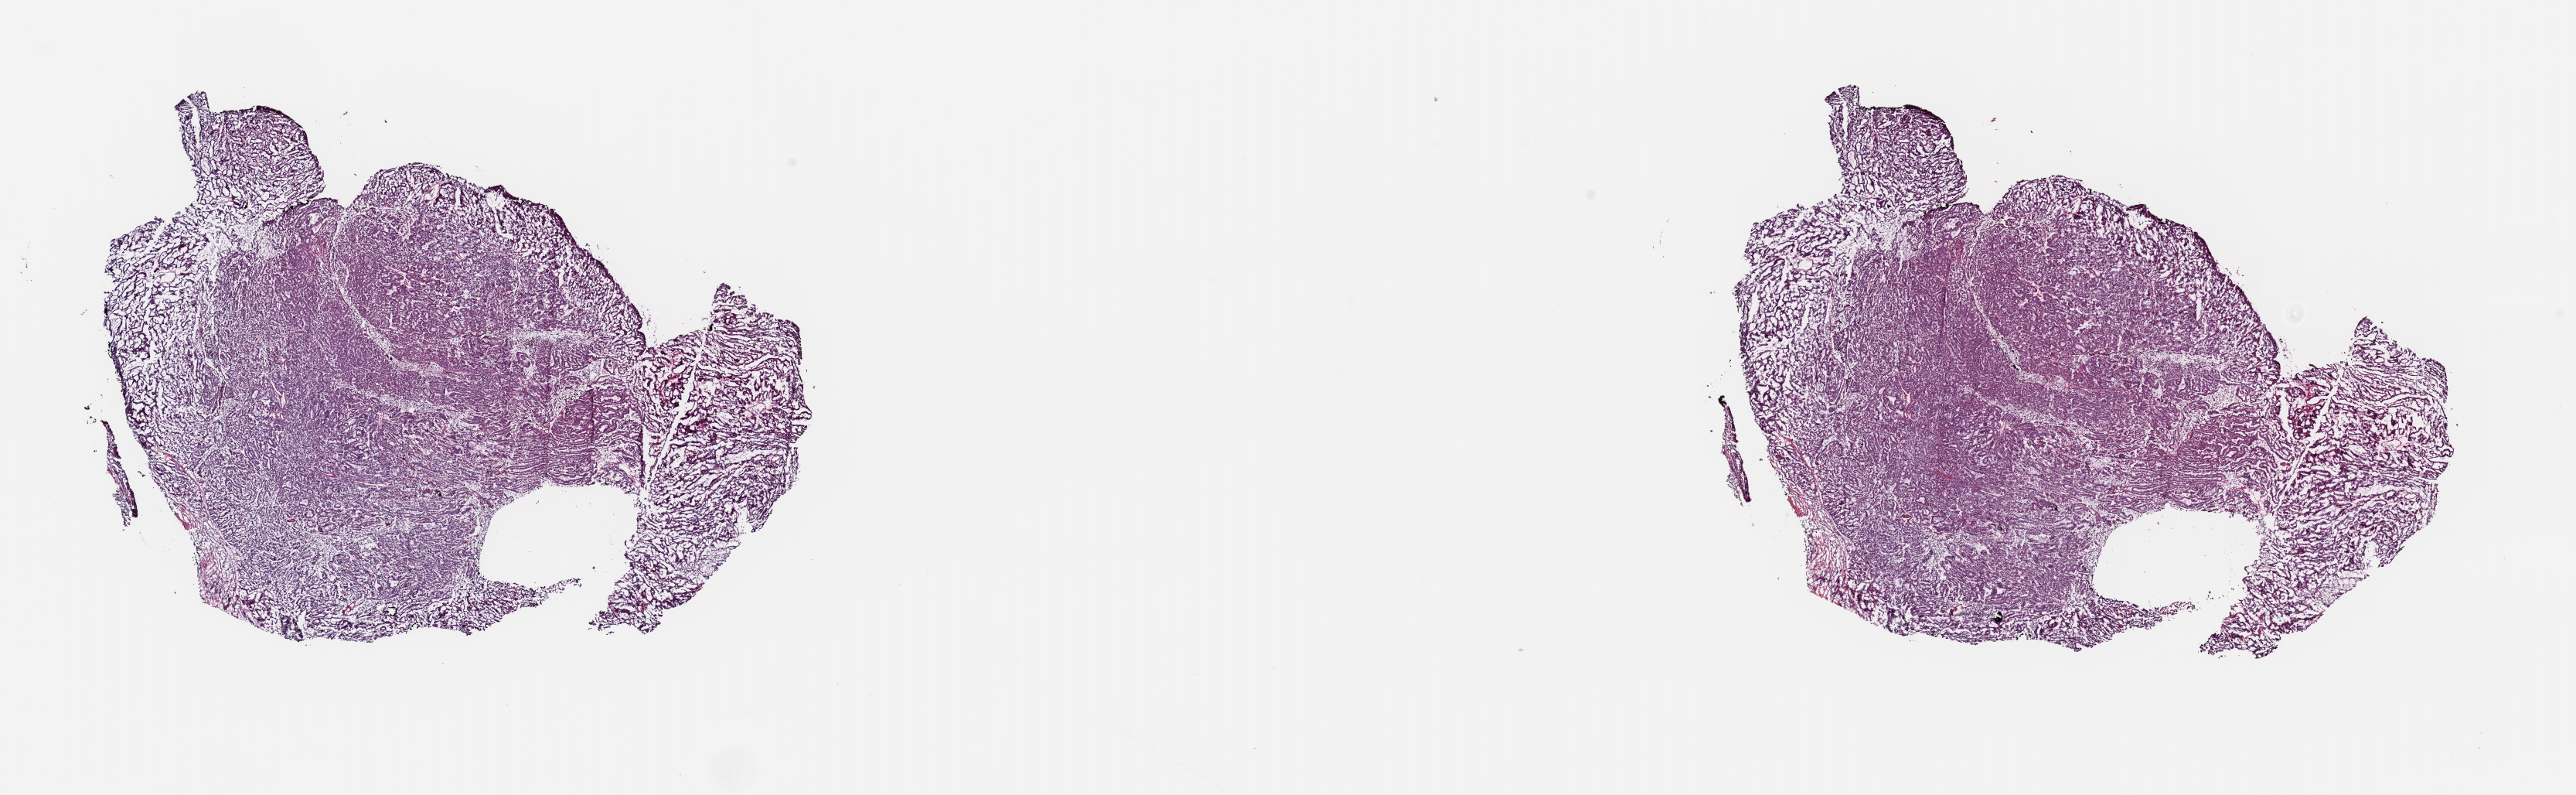
Digitized H&E-stained tissue section (whole slide), a low-resolution overview of the entire scanned area, about 26.3 x 8.1 mm (slide scanned at 40x), frozen section from the top of the tissue portion, sample: primary tumour, thyroid. Patient: female, age at initial diagnosis 33 years. Slide review estimates, as recorded: tumour cells 100%, tumour nuclei 97%, normal cells 0%, stromal cells 0%, necrosis 0%. Infiltration values recorded for this section: lymphocyte infiltration 0%, monocyte infiltration 0%, neutrophil infiltration 0%.
AJCC pathologic stage: I (6th edition). Laterality: right. Lymph nodes positive (case pathology): 0 of 8 examined. Histologic diagnosis: Papillary adenocarcinoma, NOS (thyroid gland).